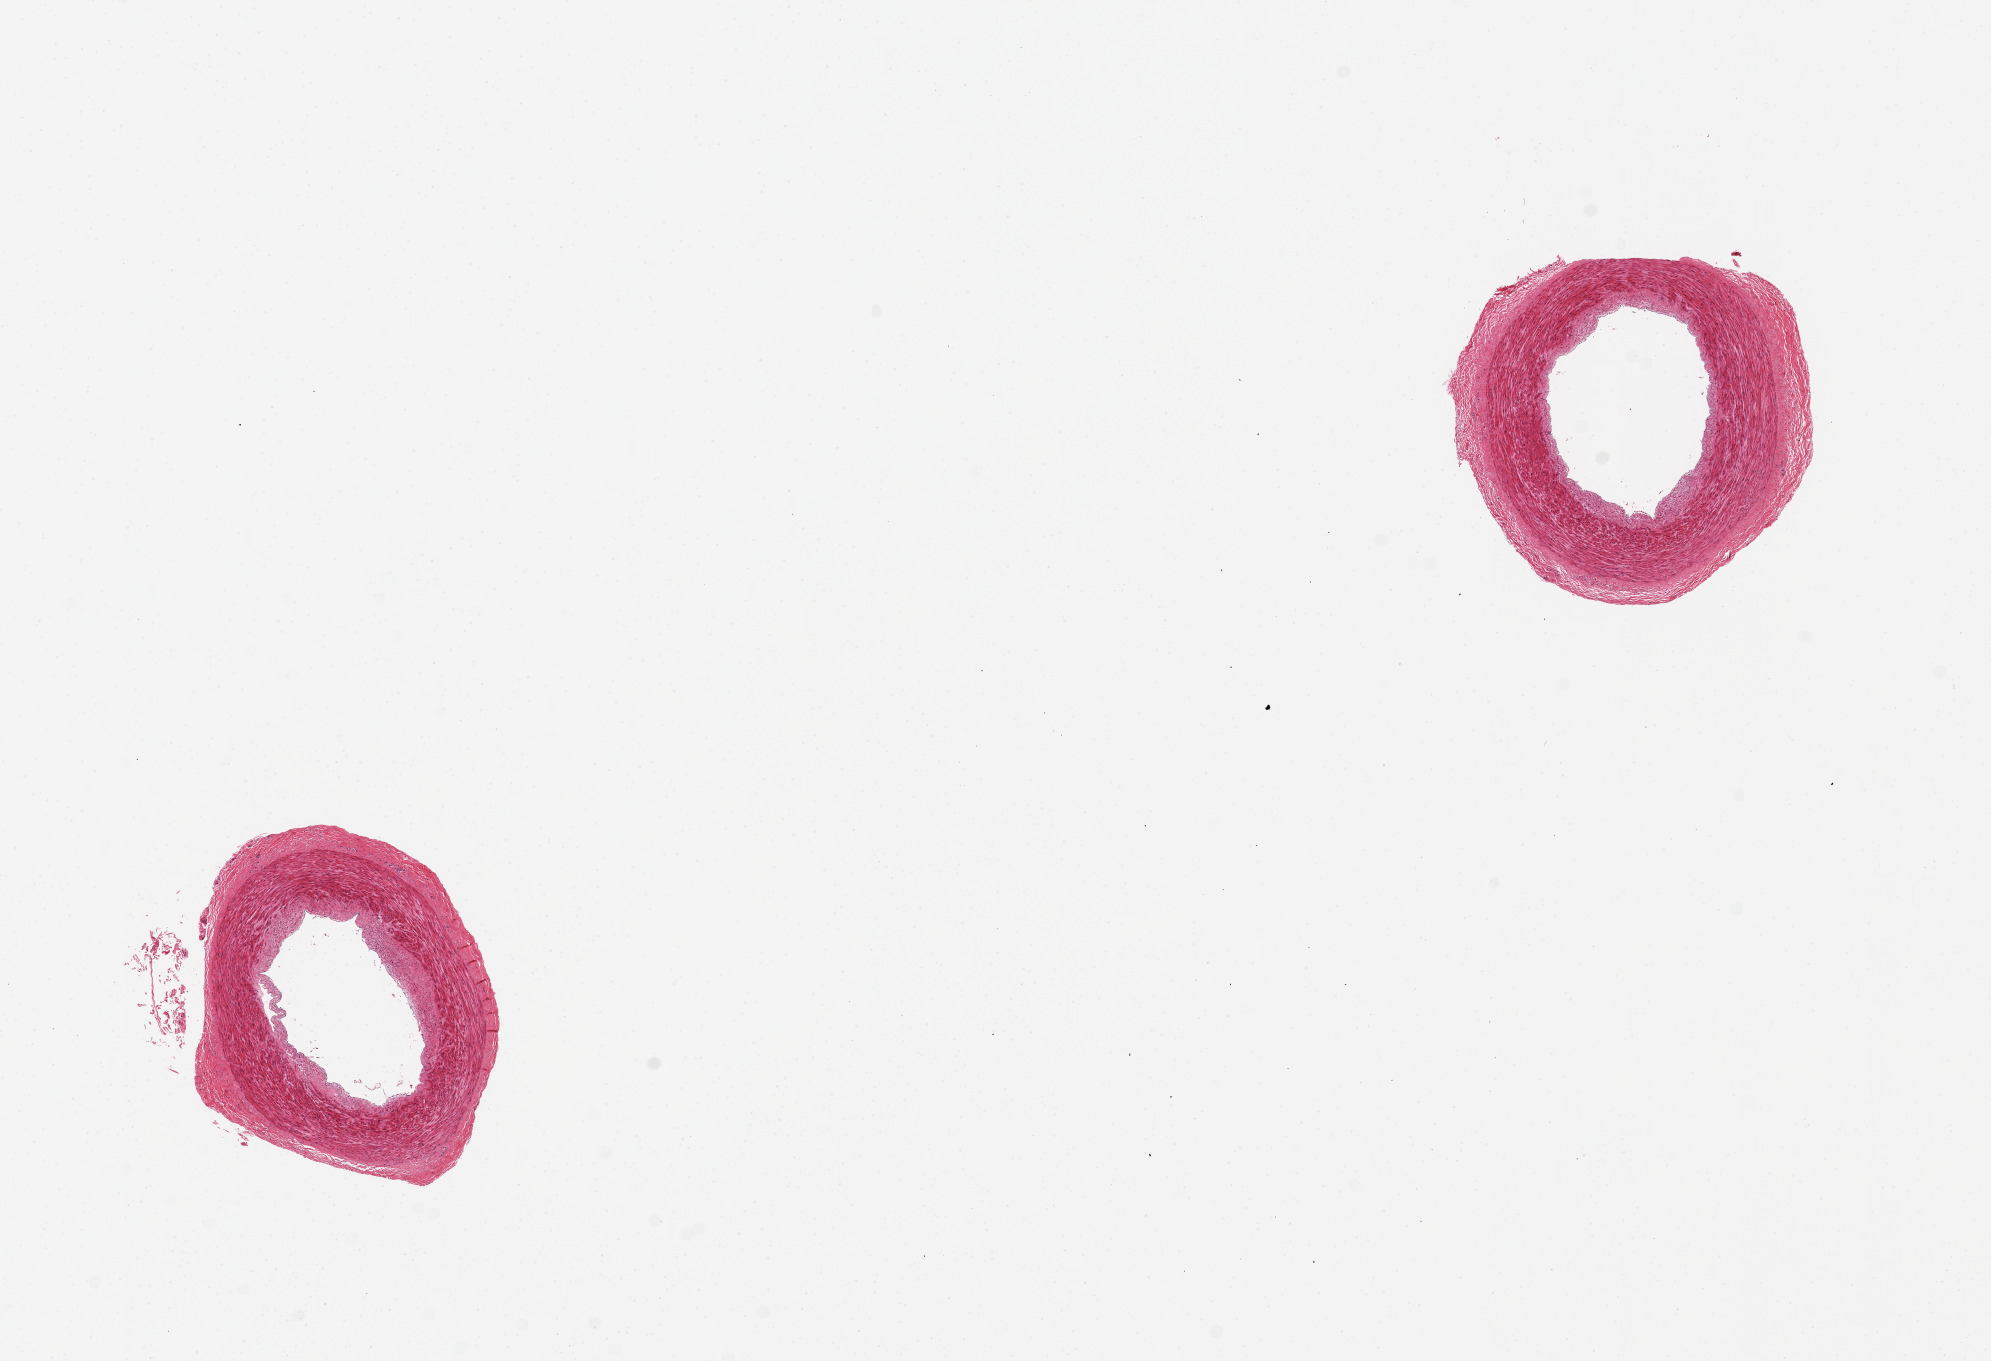
Whole-slide image, haematoxylin and eosin stain, low-resolution overview of the scanned area, about 15.8 x 10.8 mm (from a 20x scan); PAXgene-fixed paraffin-embedded (PFPE) section; section of tibial artery (target tissue); tissue donor sample. Donor sex: male.
- pathologist's review note for this sample: 2 pieces, well-trimmed